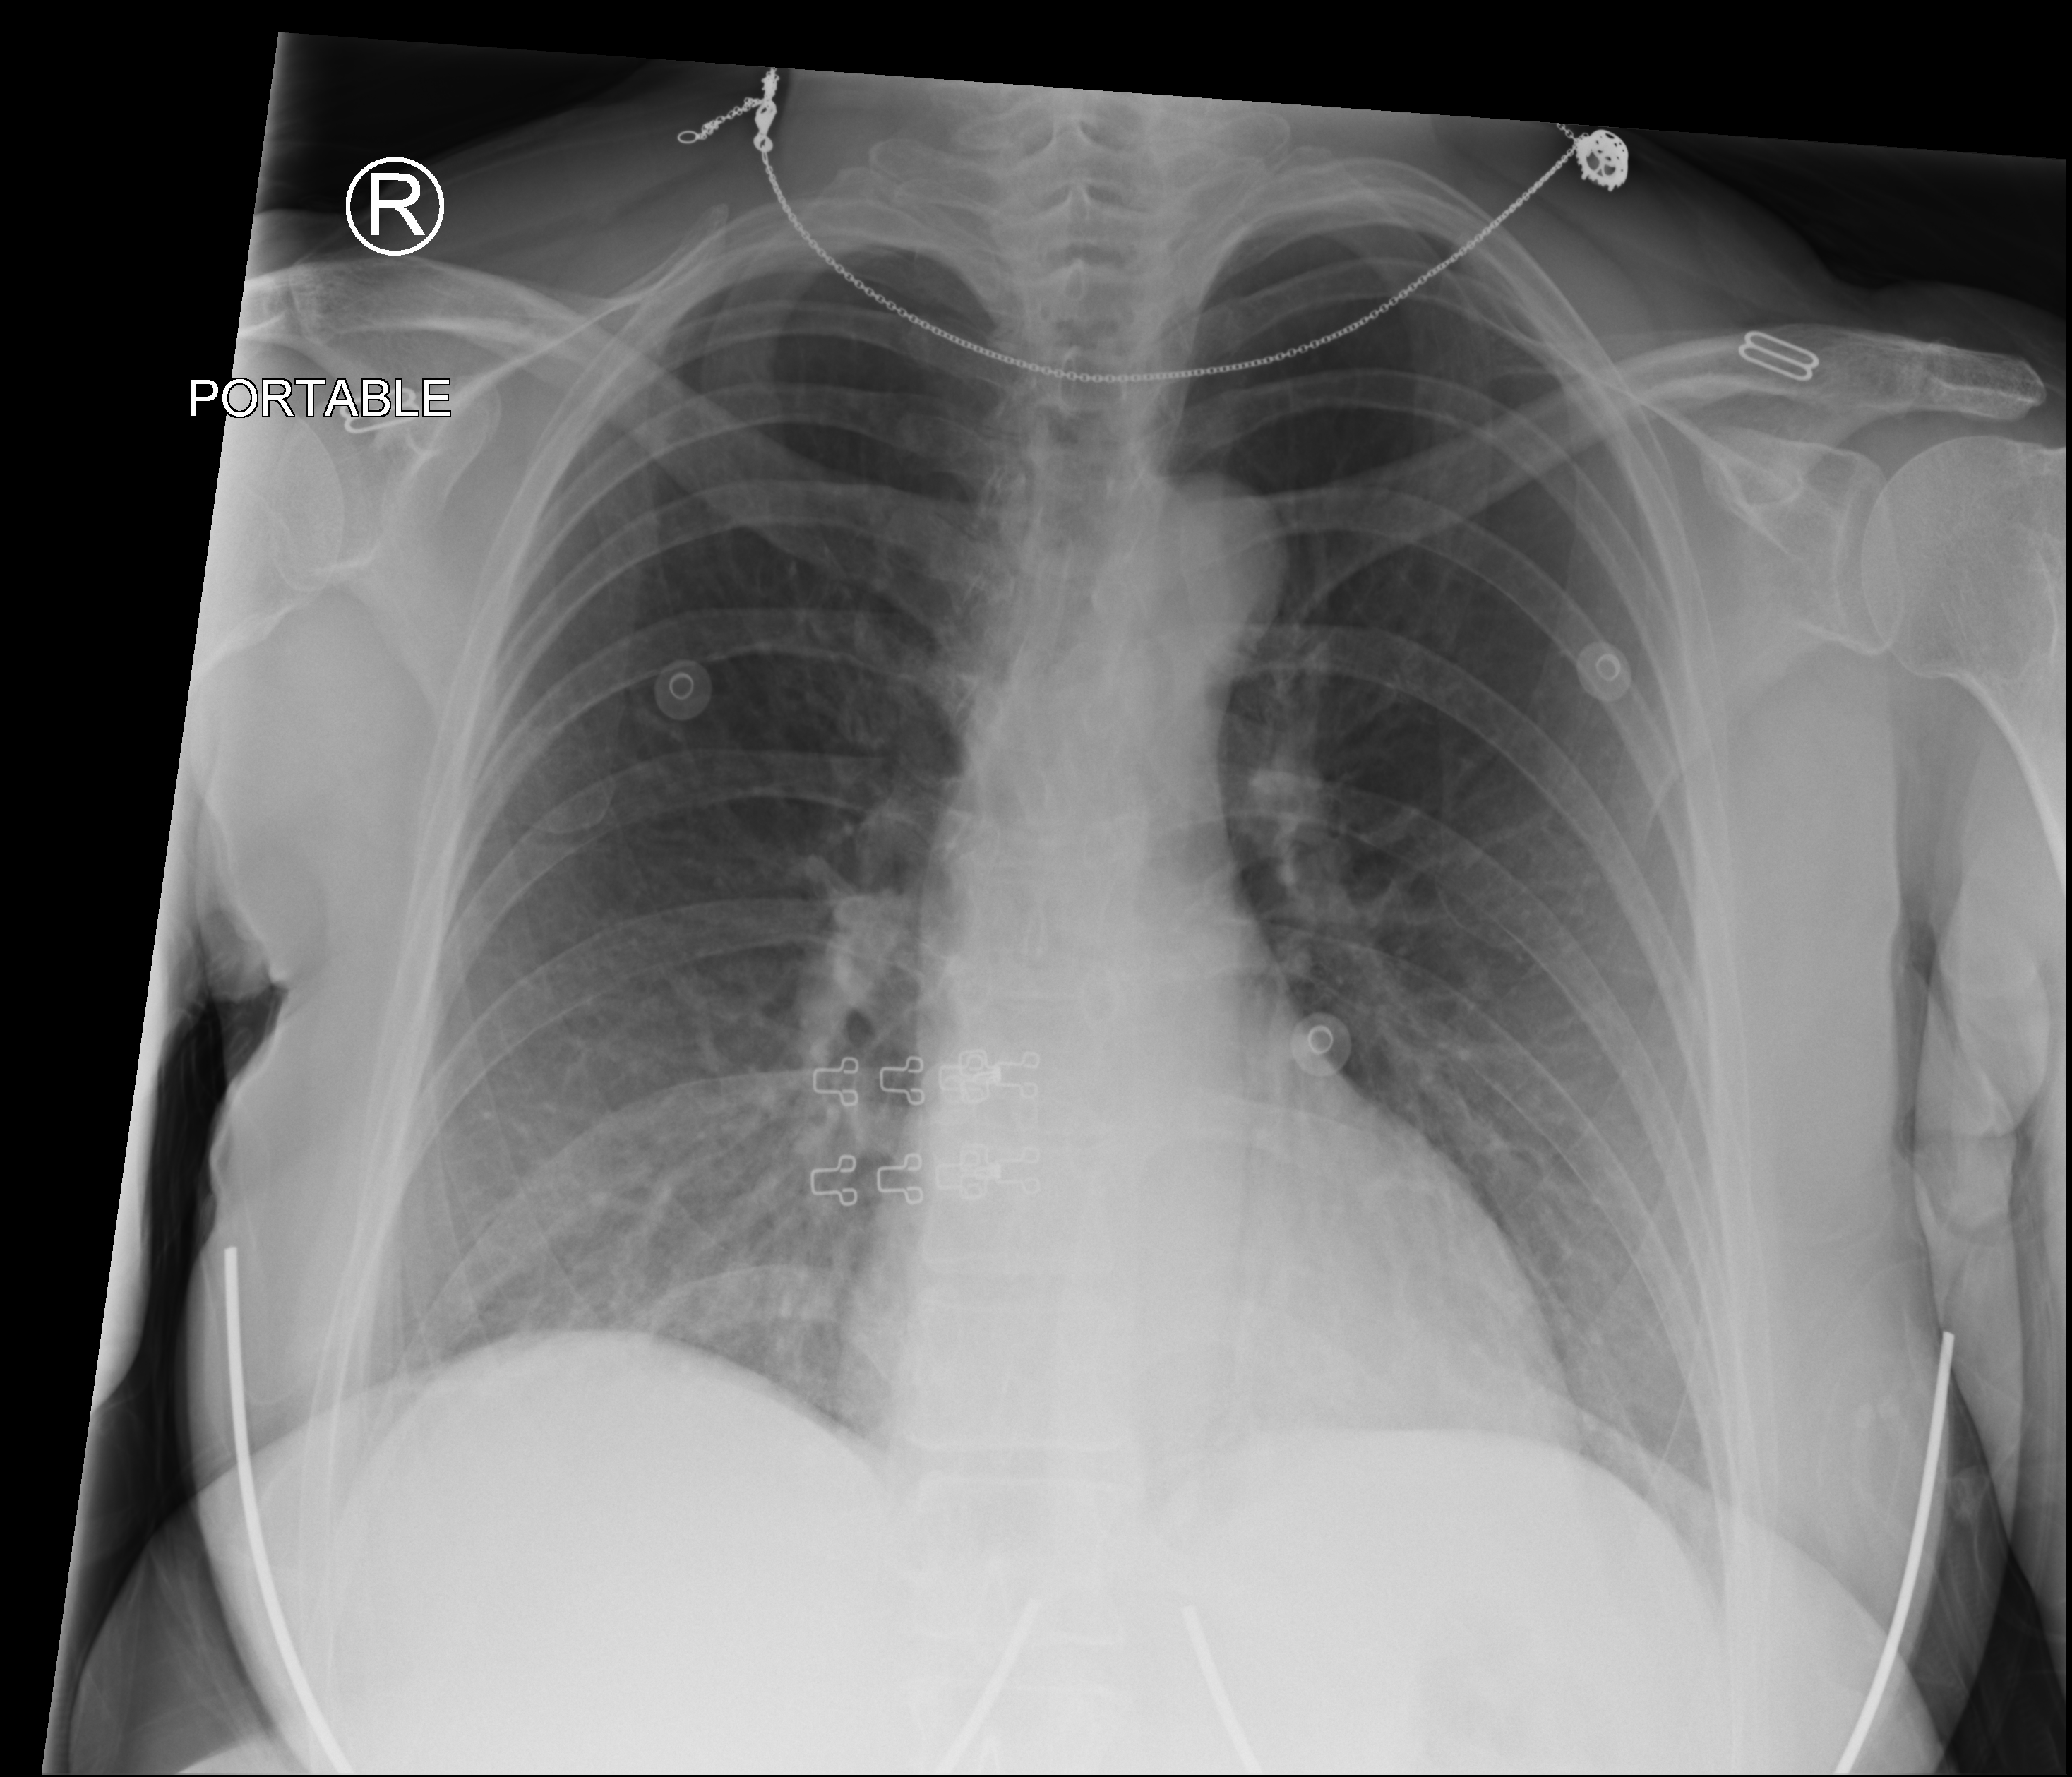
Bedside chest radiograph (computed radiography), anteroposterior (AP) projection. Patient hospitalised with COVID-19; female, aged 18–59 years.
Admission-level facts for this patient (not findings on this image; timing relative to this image not recorded): admitted to intensive care during this hospital stay: no.